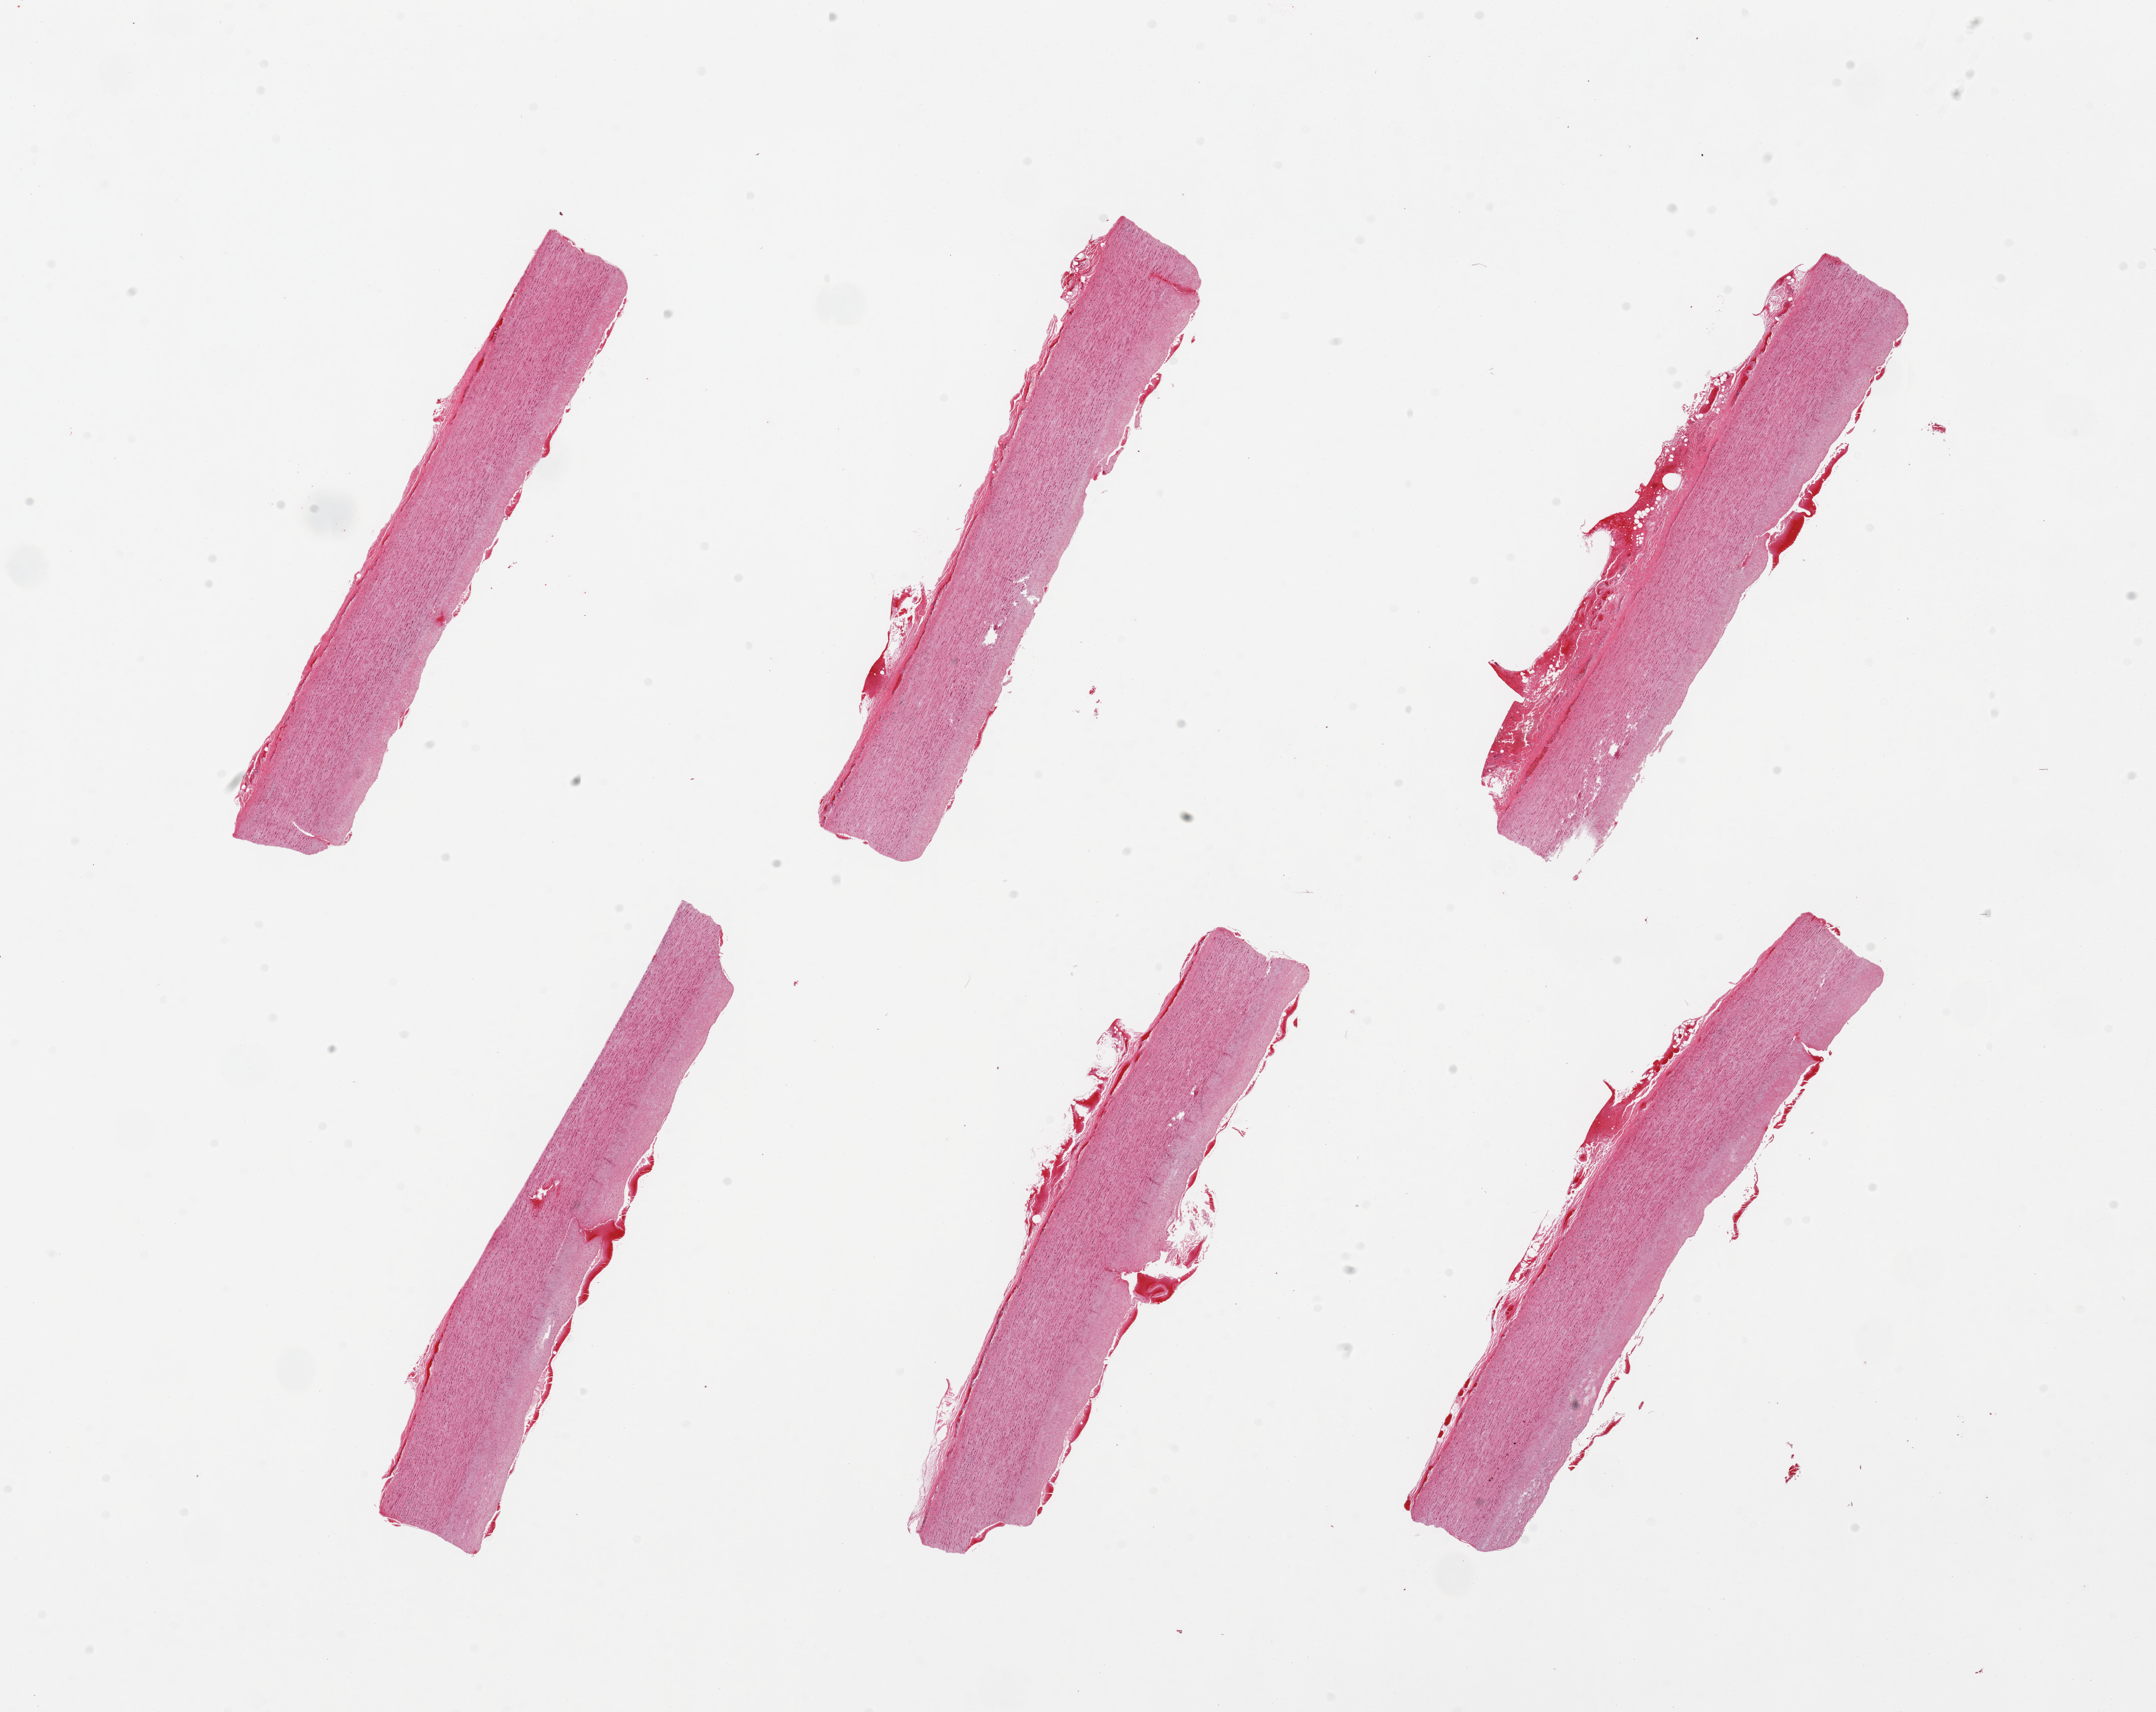
Whole-slide image, H&E stain, a low-resolution overview of the entire scanned area, about 25.6 x 20.3 mm (acquisition: 20x scan); PAXgene-fixed paraffin-embedded (PFPE) section; section of aorta (target tissue); tissue donor sample. Donor: male.
Review note (as recorded): 6 pieces, adherent serosa/fat up to ~0.5mm on several sections.